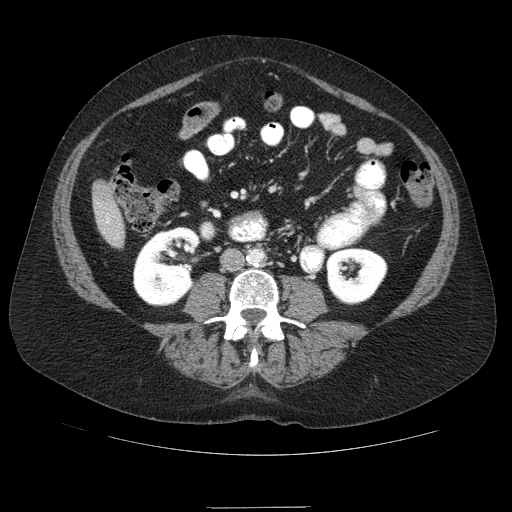
Contrast-enhanced abdominal CT (liver protocol), one axial slice; position 13 of 89 along the scan axis; soft-tissue window (W 400 / L 40 HU); 2.5 mm slice thickness; 512 × 512 image matrix. From the clinical record (not read from this slice): diagnosis: hepatocellular carcinoma (patient treated with transarterial chemoembolisation; whether this scan precedes or follows treatment is not stated here); TNM stage (as recorded): Stage-IIIB; Child-Pugh class: A.
Structures marked on this image (semi-automatic segmentation, software-assisted and operator-edited):
- liver parenchyma outside the tumour (the mass and vessels are separate outlines, so this box may not span the whole liver): bounding box [x1, y1, x2, y2] px = [92, 180, 124, 248]
- liver vessels: [106, 218, 109, 223]